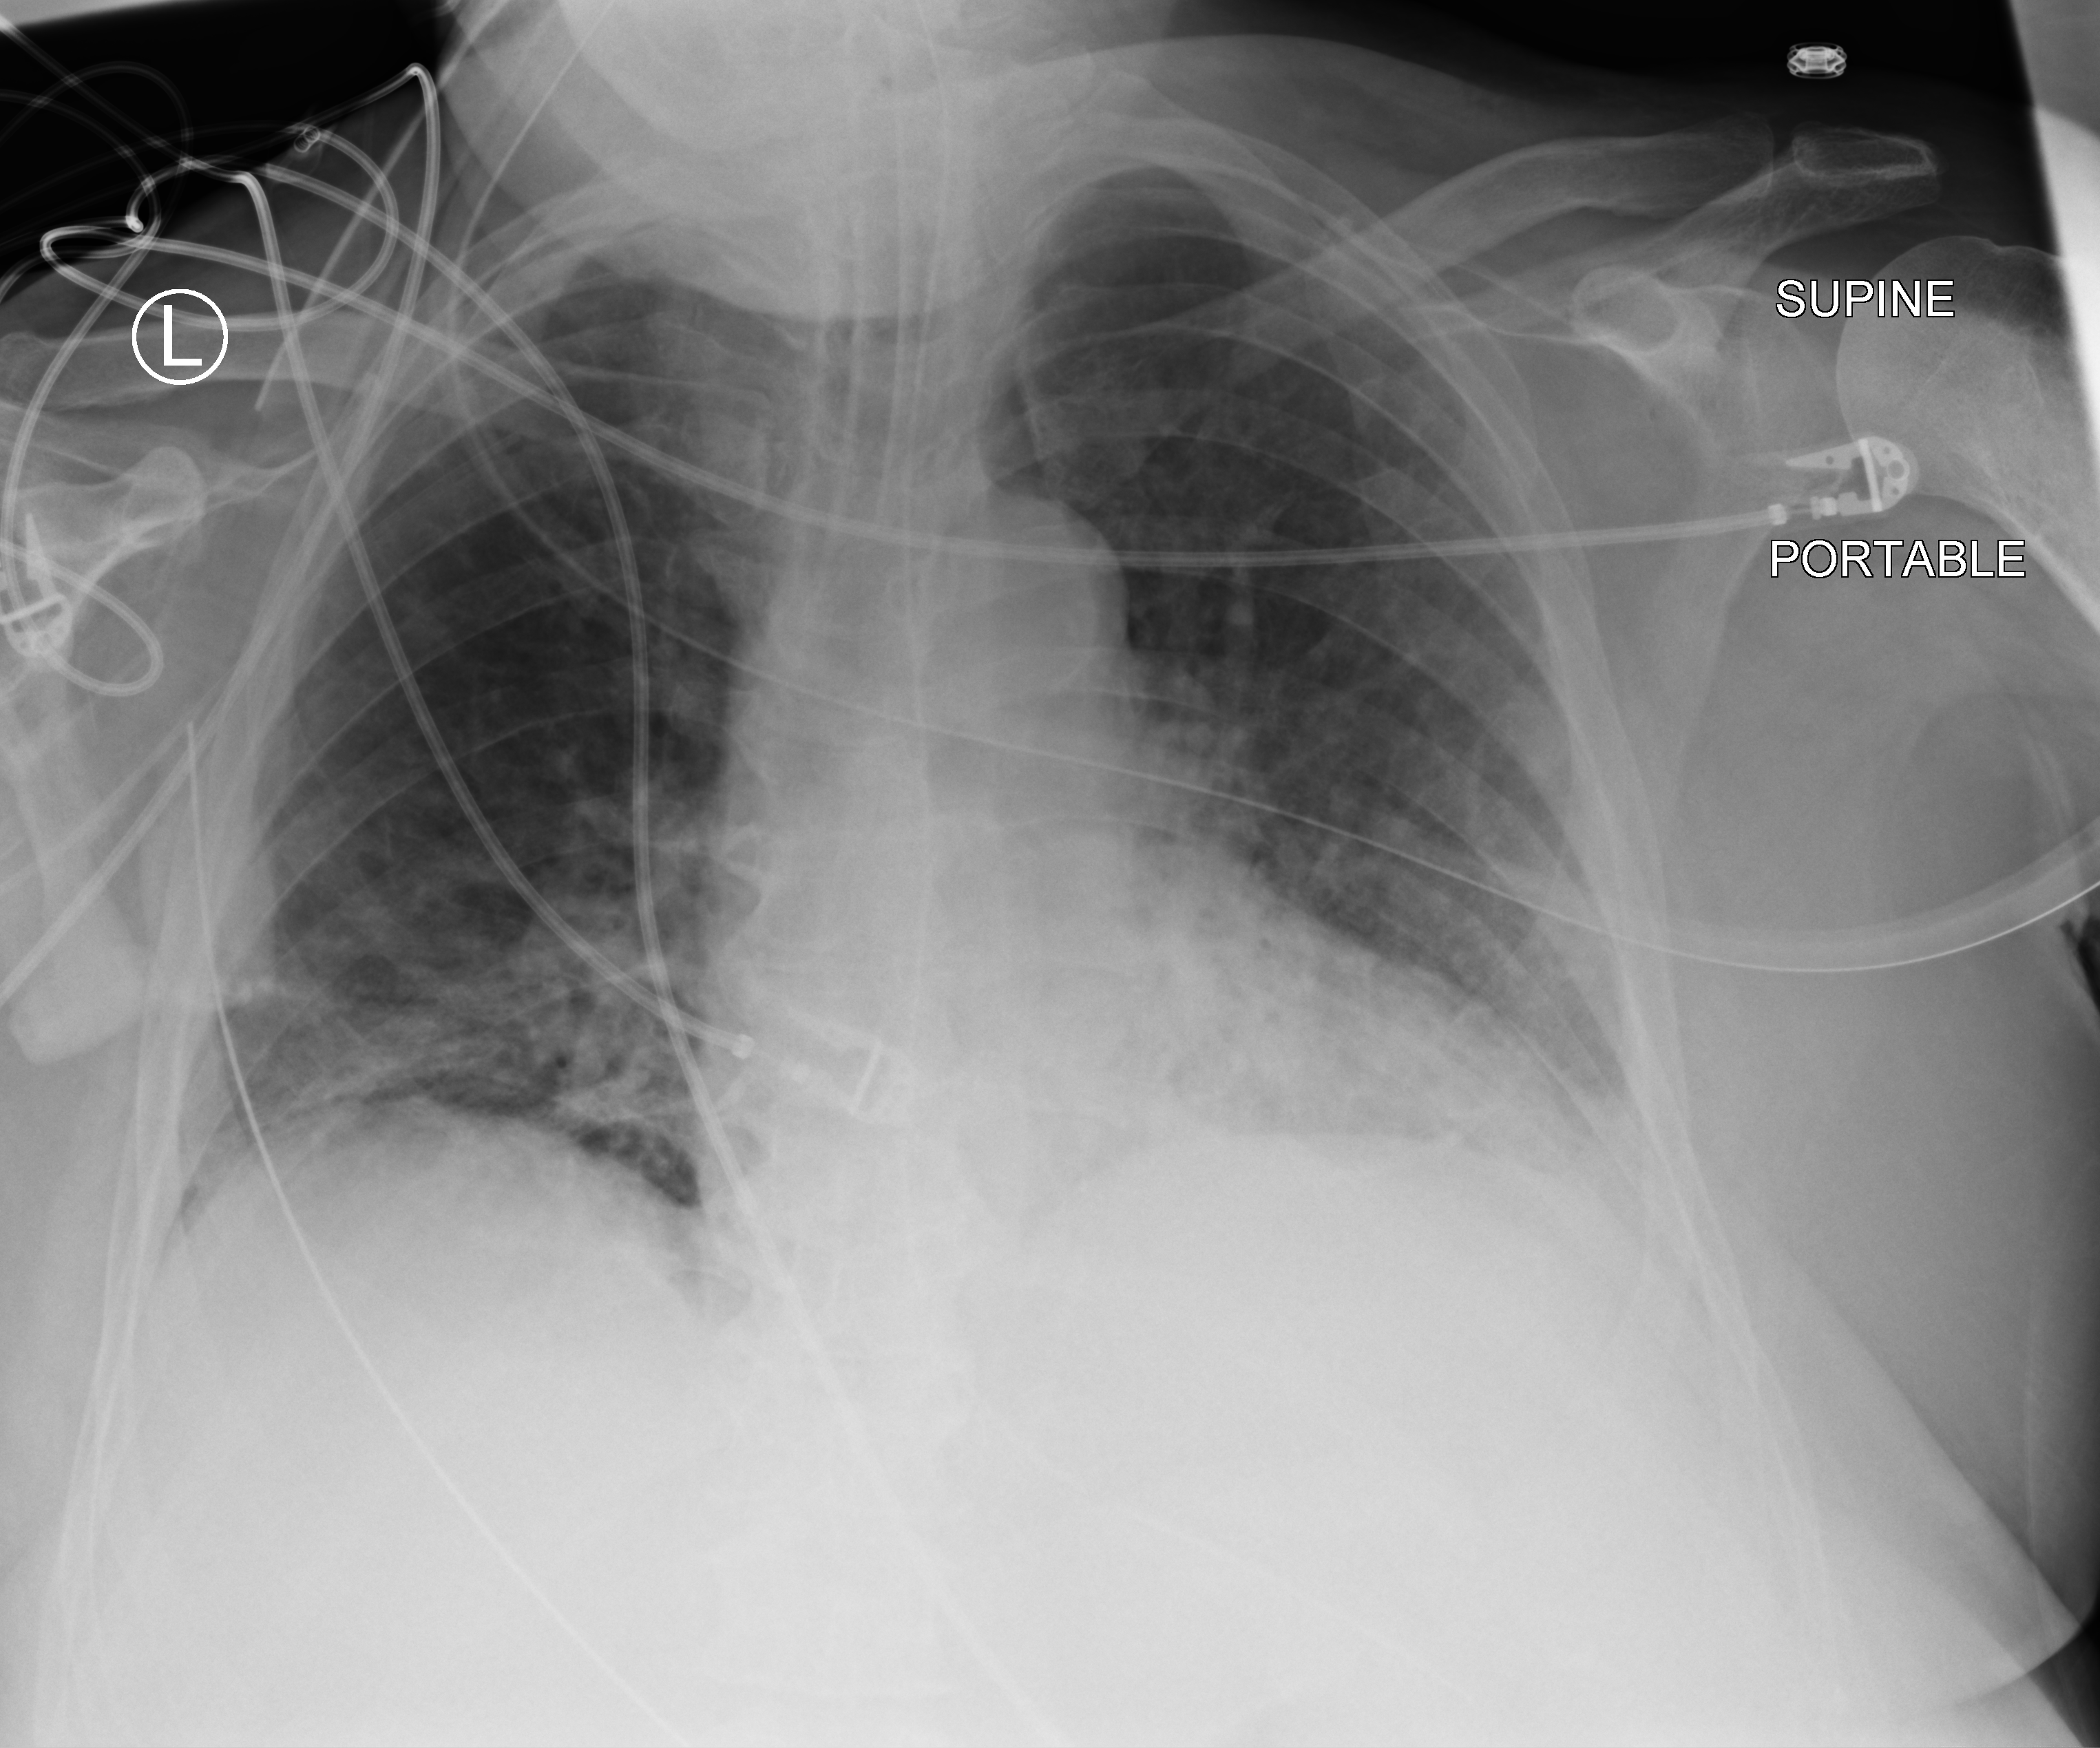
Portable chest radiograph, anteroposterior (AP) projection. Patient hospitalised with COVID-19; male, aged 60–74 years.
Admission-level facts for this patient (not findings on this image; timing relative to this image not recorded): admitted to intensive care during this hospital stay: yes; smoking status (admission record): never.